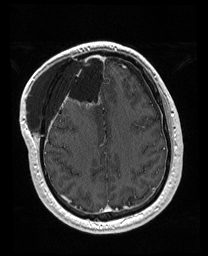
Brain MRI from a brain-tumour surgery series, one axial slice. Slice 63 of 176 in the series (ordered by position). T1-weighted post-contrast. 208 × 256 image matrix. Case-level facts recorded for this patient, not image findings: histopathology: Astrocytoma; WHO grade: 4; IDH mutation: yes; tumour location: Right Orbitofrontal Anterior Temporal Insular.
Structures marked on this image (manually delineated by an expert):
- previous resection cavity: bounding box (x1, y1, x2, y2) in pixels: (56, 52, 106, 111)